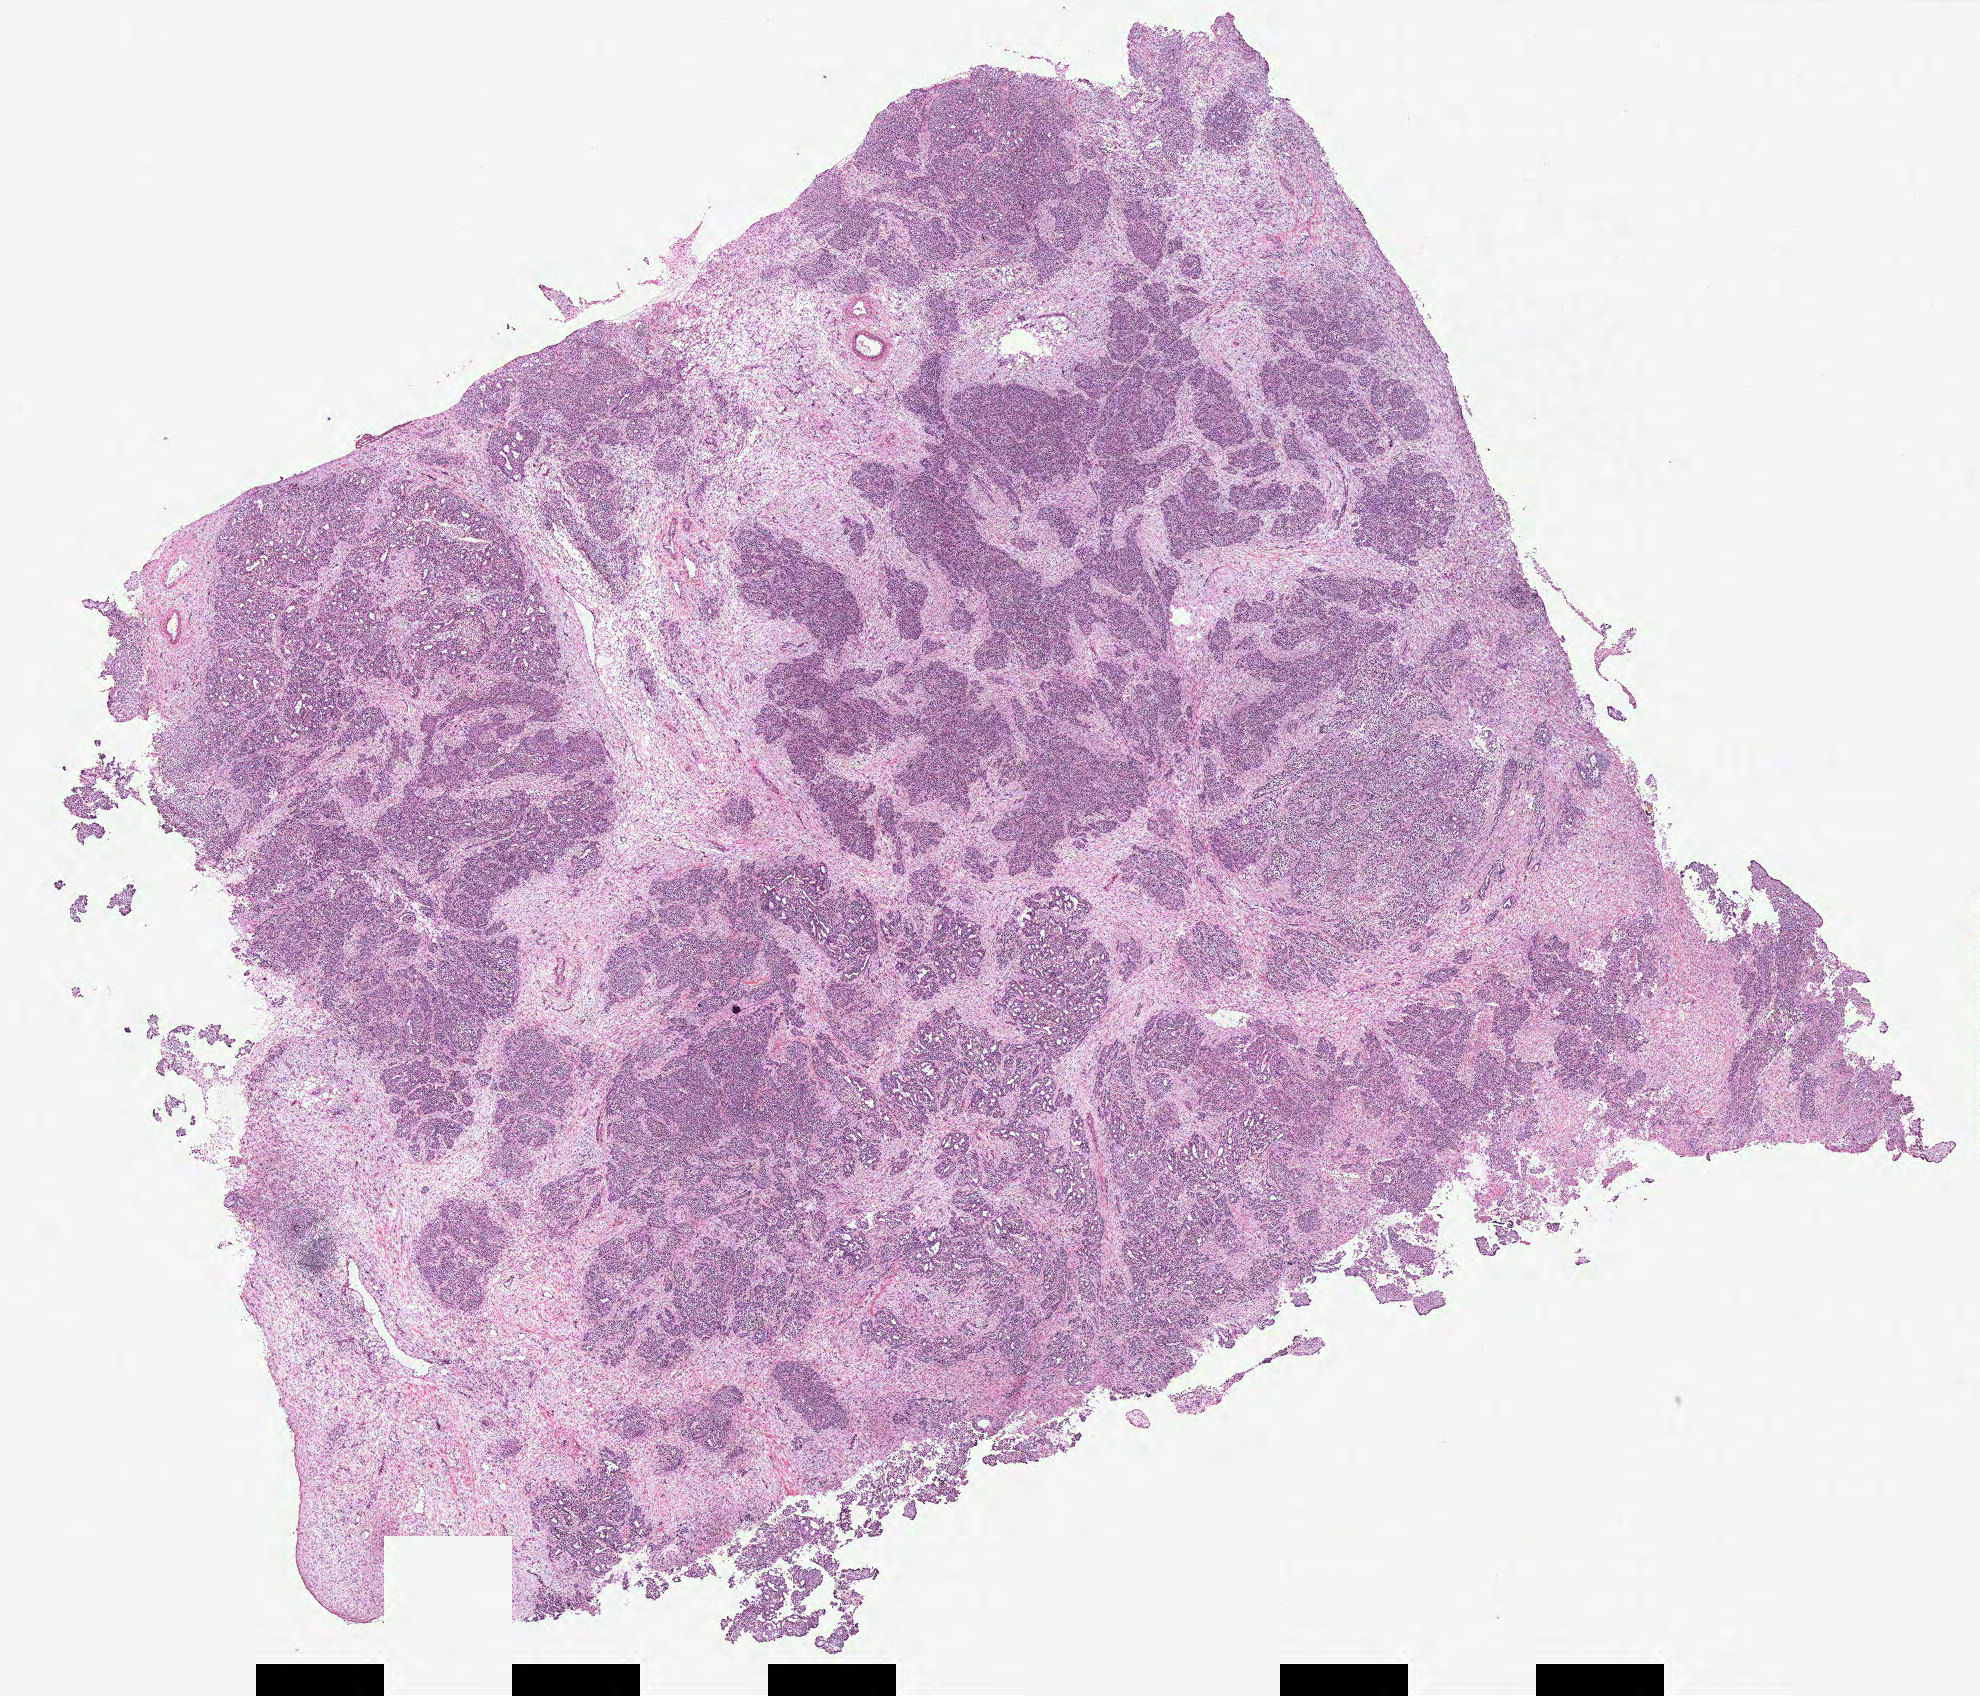
Whole-slide histology image, H&E — whole scanned area (about 15.8 x 13.6 mm) shown as a low-resolution overview; tumour tissue sample, ovary. Patient: female, age 37 years.
• primary tumour site (as recorded): ovary
• histologic diagnosis: Serous adenocarcinoma, NOS